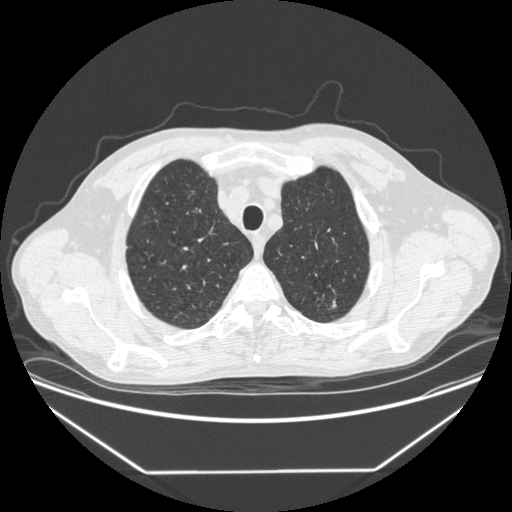
Low-dose screening chest CT, one axial slice. Slice 331 of 383 in the series (ordered by position). Reconstruction kernel STANDARD. 120 kVp. Lung window (W 1500 / L -600 HU). 512 × 512 image matrix.
Structures marked on this image (outlined manually by an expert reader):
- lesion 1 (tumor, upper lobe of left lung): box from (x=332, y=300) to (x=337, y=308) px